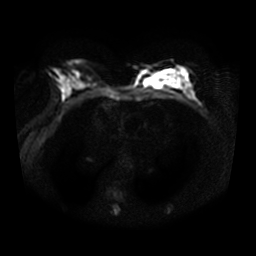
Breast MRI, one axial slice. Slice 16 of 32 in the series (ordered by position). Diffusion-weighted series; image 2 of 4 stored at this slice position (different b-values; order by instance number). 3 T. 256 × 256 image matrix. Female patient.
Annotated regions visible in this slice (outlined manually by an expert reader):
- tumour on diffusion-weighted imaging: bounding box [x1, y1, x2, y2] px = [144, 72, 182, 88]